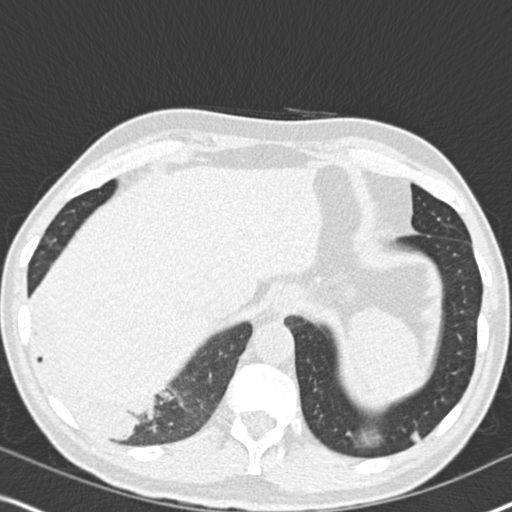
Chest CT (low-dose screening protocol), one axial image; second screening round (one year after baseline); lung window (W 1500 / L -600 HU); 2 mm slice thickness; standard (soft-tissue) reconstruction kernel (B30f); slice 135 of 182 in the series. Male, age 61 years at enrolment. Current smoker at enrolment.
• Expert-annotated lung lesion, bounding box <14,272,179,453> (left, top, right, bottom; pixels).
• Reader record for this screening exam (exam-level; its link to the box is not recorded): non-calcified nodule or mass ≥4 mm, right lower lobe, 90 × 80 mm, soft tissue attenuation, pre-existing on the prior screen: yes; interval growth: yes.
• Later outcome: lung cancer diagnosed 20 days after this screen — bronchiolo-alveolar adenocarcinoma, NOS, right lower lobe, moderately differentiated (G2), stage IIIB (AJCC 6th edition), 90 mm at pathology.